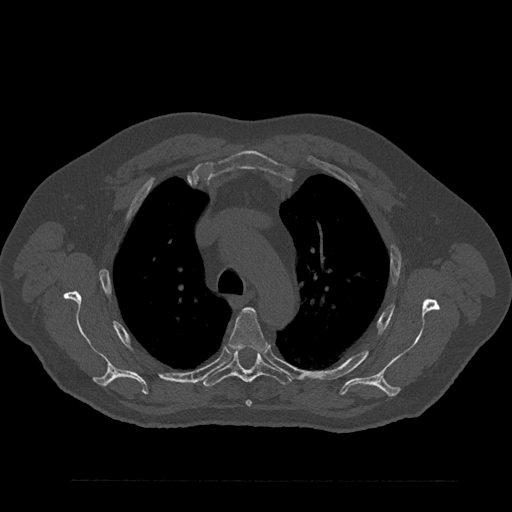
CT including the spine, one axial slice; slice 622 of 797 in the series (ordered by position); reconstruction kernel Br40s/3; 120 kVp; bone window (W 1800 / L 400 HU); 0.5 mm slice thickness; 512 × 512 image matrix, field of view 430 × 430 mm. Male patient, age 61 years. Case-level facts recorded for this patient, not image findings: primary cancer: prostate.
Structures marked on this image (semi-automatic segmentation, software-assisted and operator-edited):
- T4 vertebra: bounding box (x1, y1, x2, y2) in pixels: (228, 307, 267, 407)
- T5 vertebra: (201, 351, 291, 387)